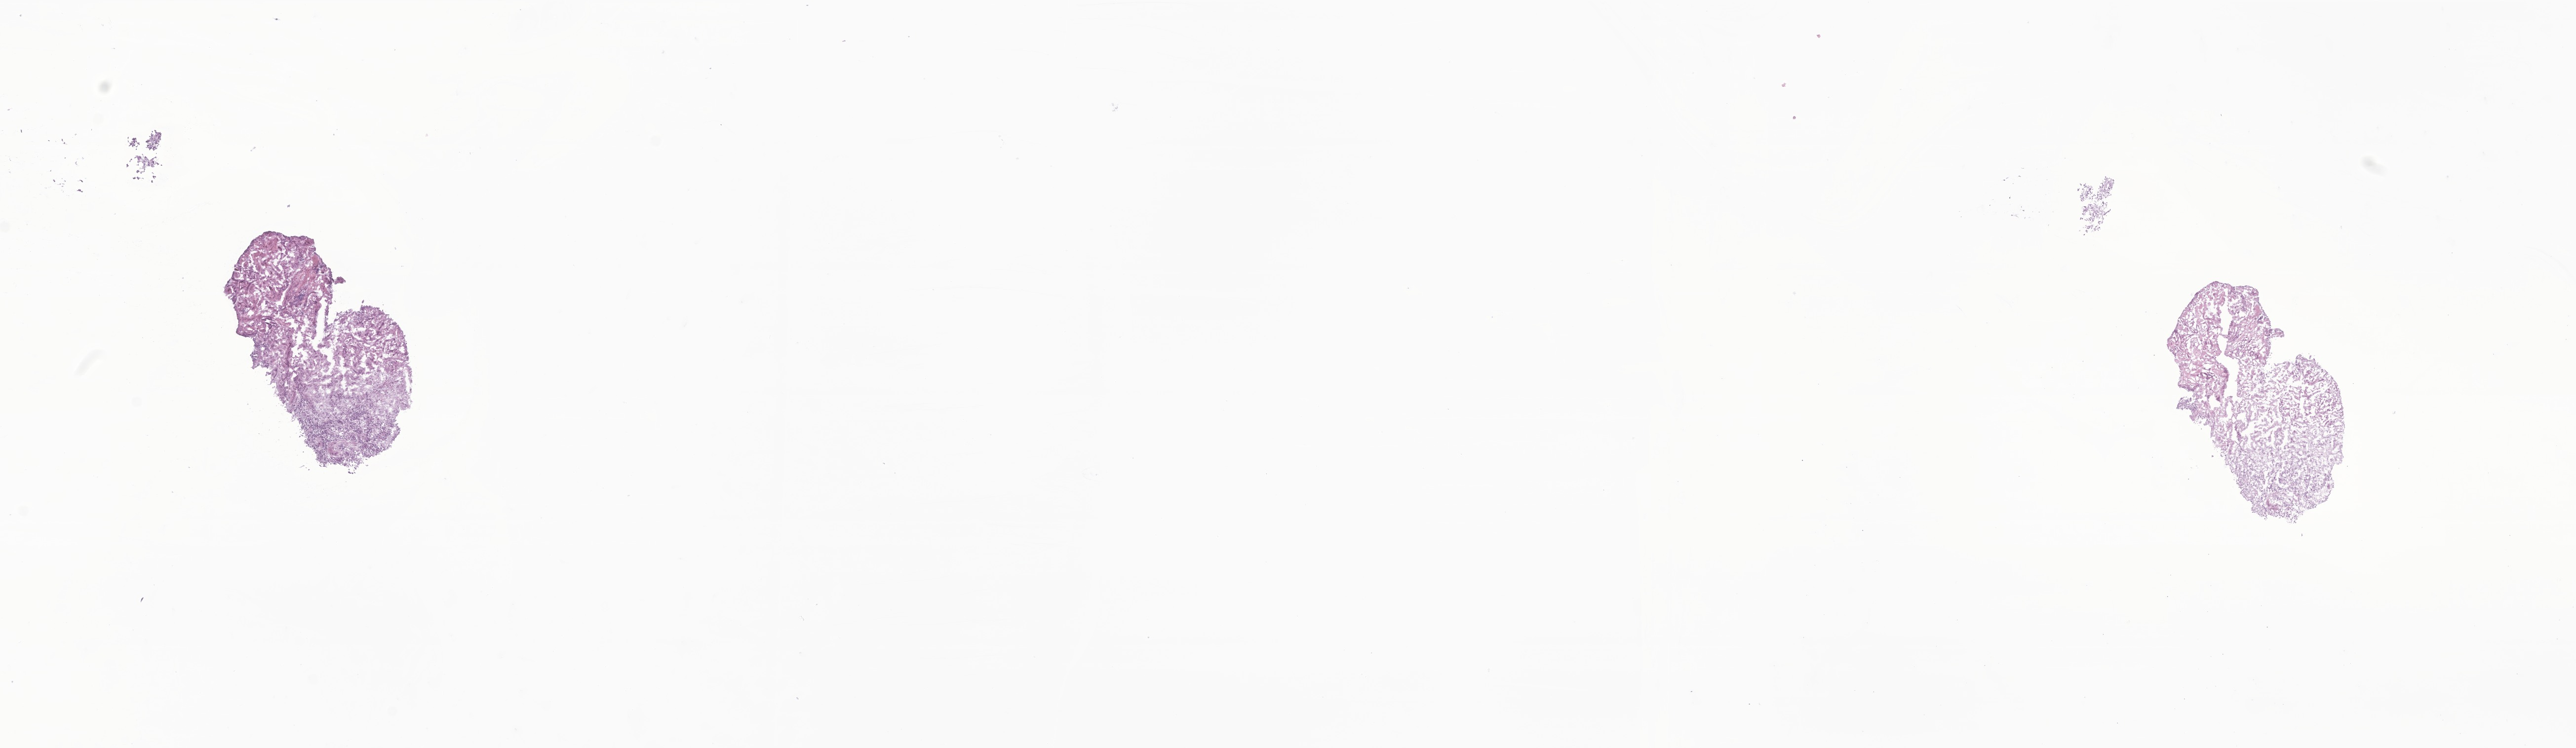
Digitized haematoxylin and eosin-stained section of tumor tissue from the spinal cord, low-resolution overview of the scanned area, about 22.0 x 6.4 mm. Frozen section (OCT-embedded). Patient: male, age 146 months (12 years 2 months).
Diagnosis (ICD-O-3 morphology term): Myxopapillary ependymoma.